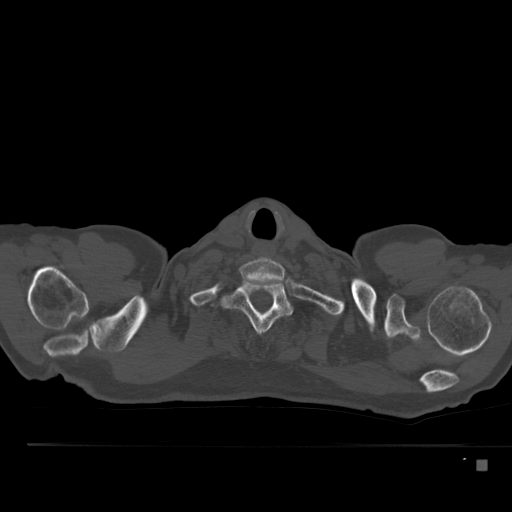
CT including the spine, one axial slice. Slice 427 of 517 in the series (ordered by position). Reconstruction kernel Br40s. 120 kVp. Bone window (W 1800 / L 400 HU). 512 × 512 image matrix, field of view 408 × 408 mm. Male patient, age 70 years. From the clinical record (not read from this slice): primary cancer: renal; vertebrae with lytic lesions (as recorded): T4, T6, T10, T12, L3, L4, L5.
Annotated regions visible in this slice (semi-automatic segmentation, software-assisted and operator-edited):
- T1 vertebra: bounding box <224,280,292,333> (left, top, right, bottom; pixels)